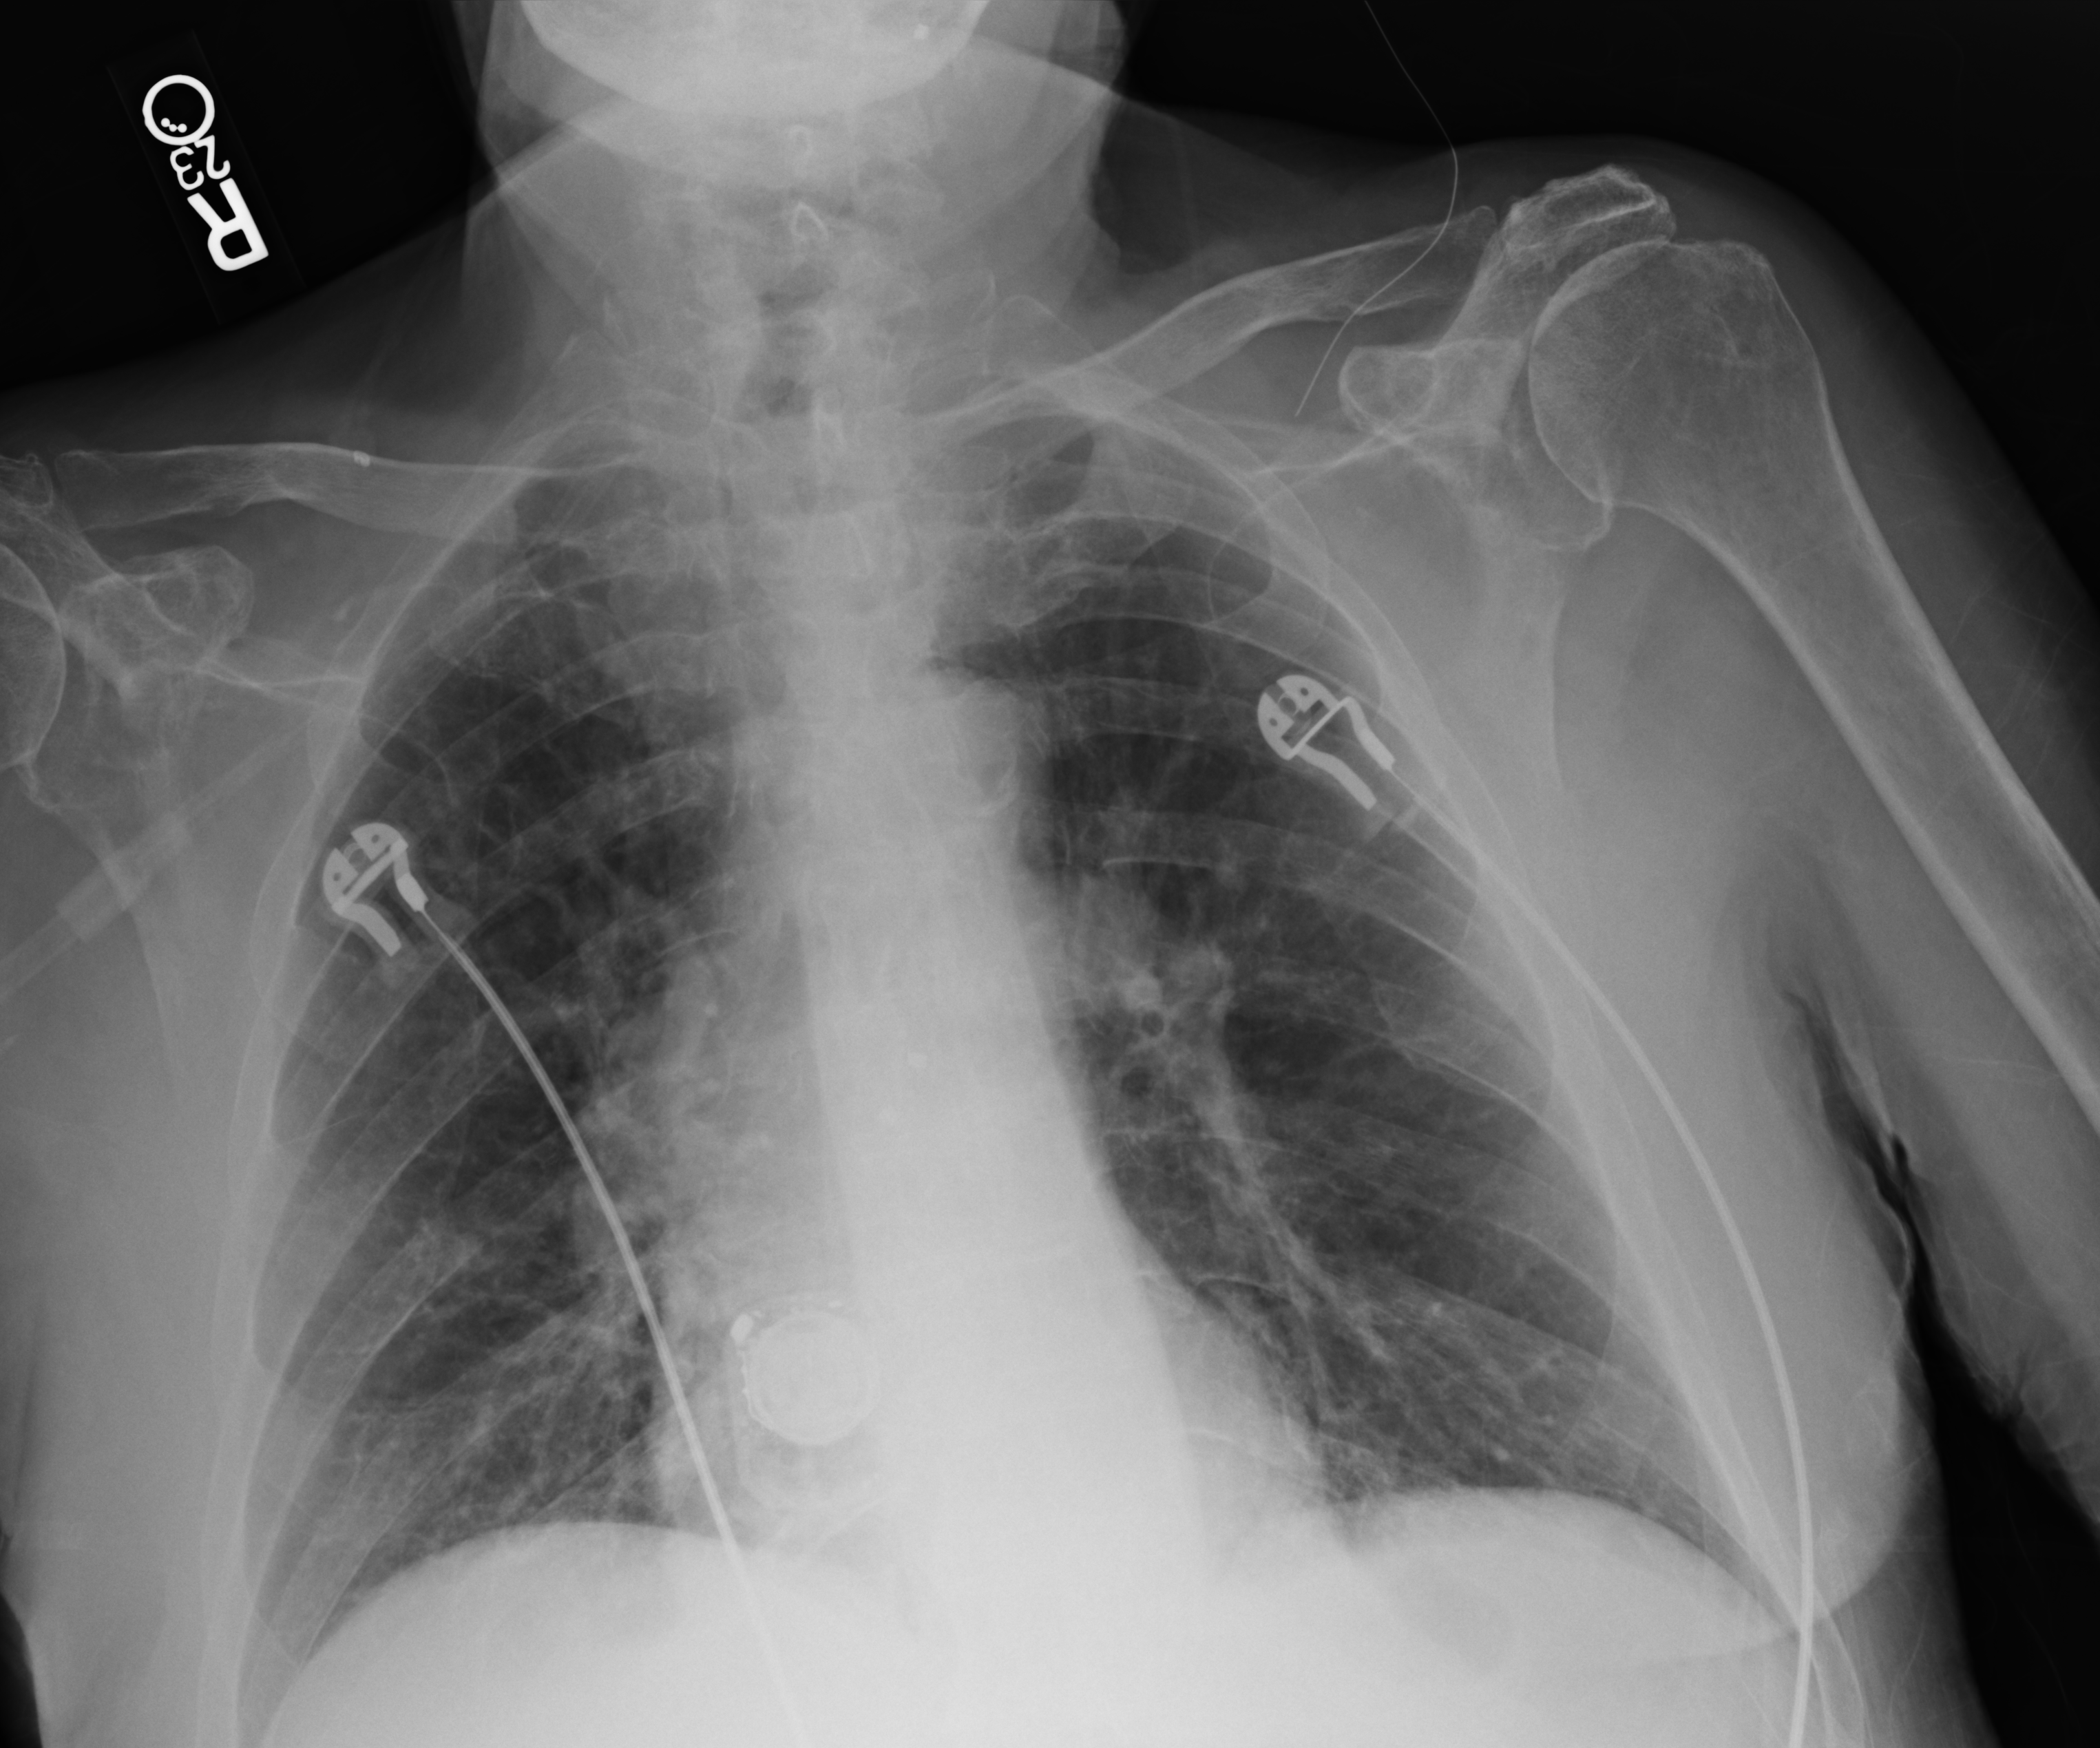
Chest X-ray (portable), anteroposterior (AP) projection. Patient hospitalised with COVID-19; male, aged 75–90 years.
Hospital-stay facts (about this admission, not read from this image; timing relative to this image not recorded): mechanically ventilated during this hospital stay: no; smoking status (admission record): former.